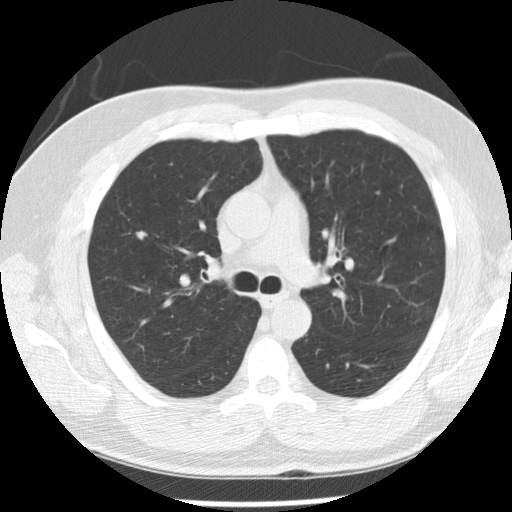
Low-dose screening chest CT, axial slice; baseline screening round; lung window (W 1500 / L -600 HU); standard (soft-tissue) reconstruction kernel (STANDARD); 512 × 512 image matrix, field of view 340 × 340 mm. Male, age 57 years at enrolment. Former smoker at enrolment.
- Lesion marked by an expert reader, bounding box (x1, y1, x2, y2) in pixels: (122, 218, 156, 252).
- The exam's reader record, not a measurement of the box and not confirmed to be the same lesion: non-calcified nodule or mass ≥4 mm, right upper lobe, 7 × 7 mm, poorly defined margins, soft tissue attenuation.
- Official screen result: positive, change unspecified: nodule(s) >= 4 mm or enlarging nodule(s), mass(es), or other non-specific abnormalities suspicious for lung cancer.
- Lung cancer was diagnosed 125 days after this screen: squamous cell carcinoma, NOS, right upper lobe, moderately differentiated (G2), stage IA (AJCC 6th edition), 10 mm at pathology.